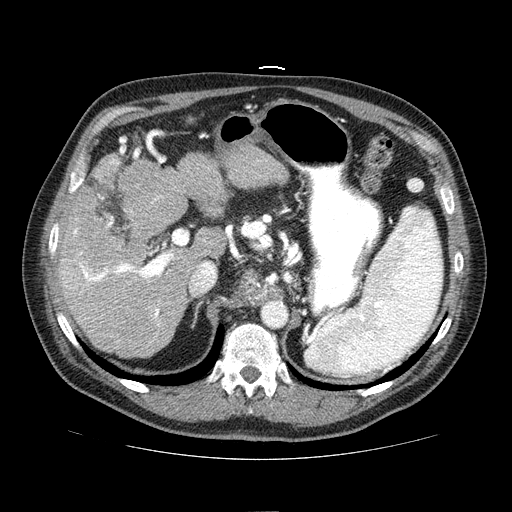
Contrast-enhanced abdominal CT (liver protocol), one axial slice; position 45 of 81 along the scan axis; reconstruction kernel STANDARD; 100 kVp; one of 2 acquisitions stored at this slice position; soft-tissue window (W 400 / L 40 HU); 2.5 mm slice thickness; 512 × 512 image matrix, field of view 400 × 400 mm. From the clinical record (not read from this slice): diagnosis: hepatocellular carcinoma (patient treated with transarterial chemoembolisation; whether this scan precedes or follows treatment is not stated here); TNM stage (as recorded): Stage-IIIA.
Annotated regions visible in this slice (semi-automatically segmented with operator editing):
- liver parenchyma outside the tumour (the mass and vessels are separate outlines, so this box may not span the whole liver): bounding box (x1, y1, x2, y2) in pixels: (58, 144, 287, 358)
- liver vessels: (62, 159, 205, 326)